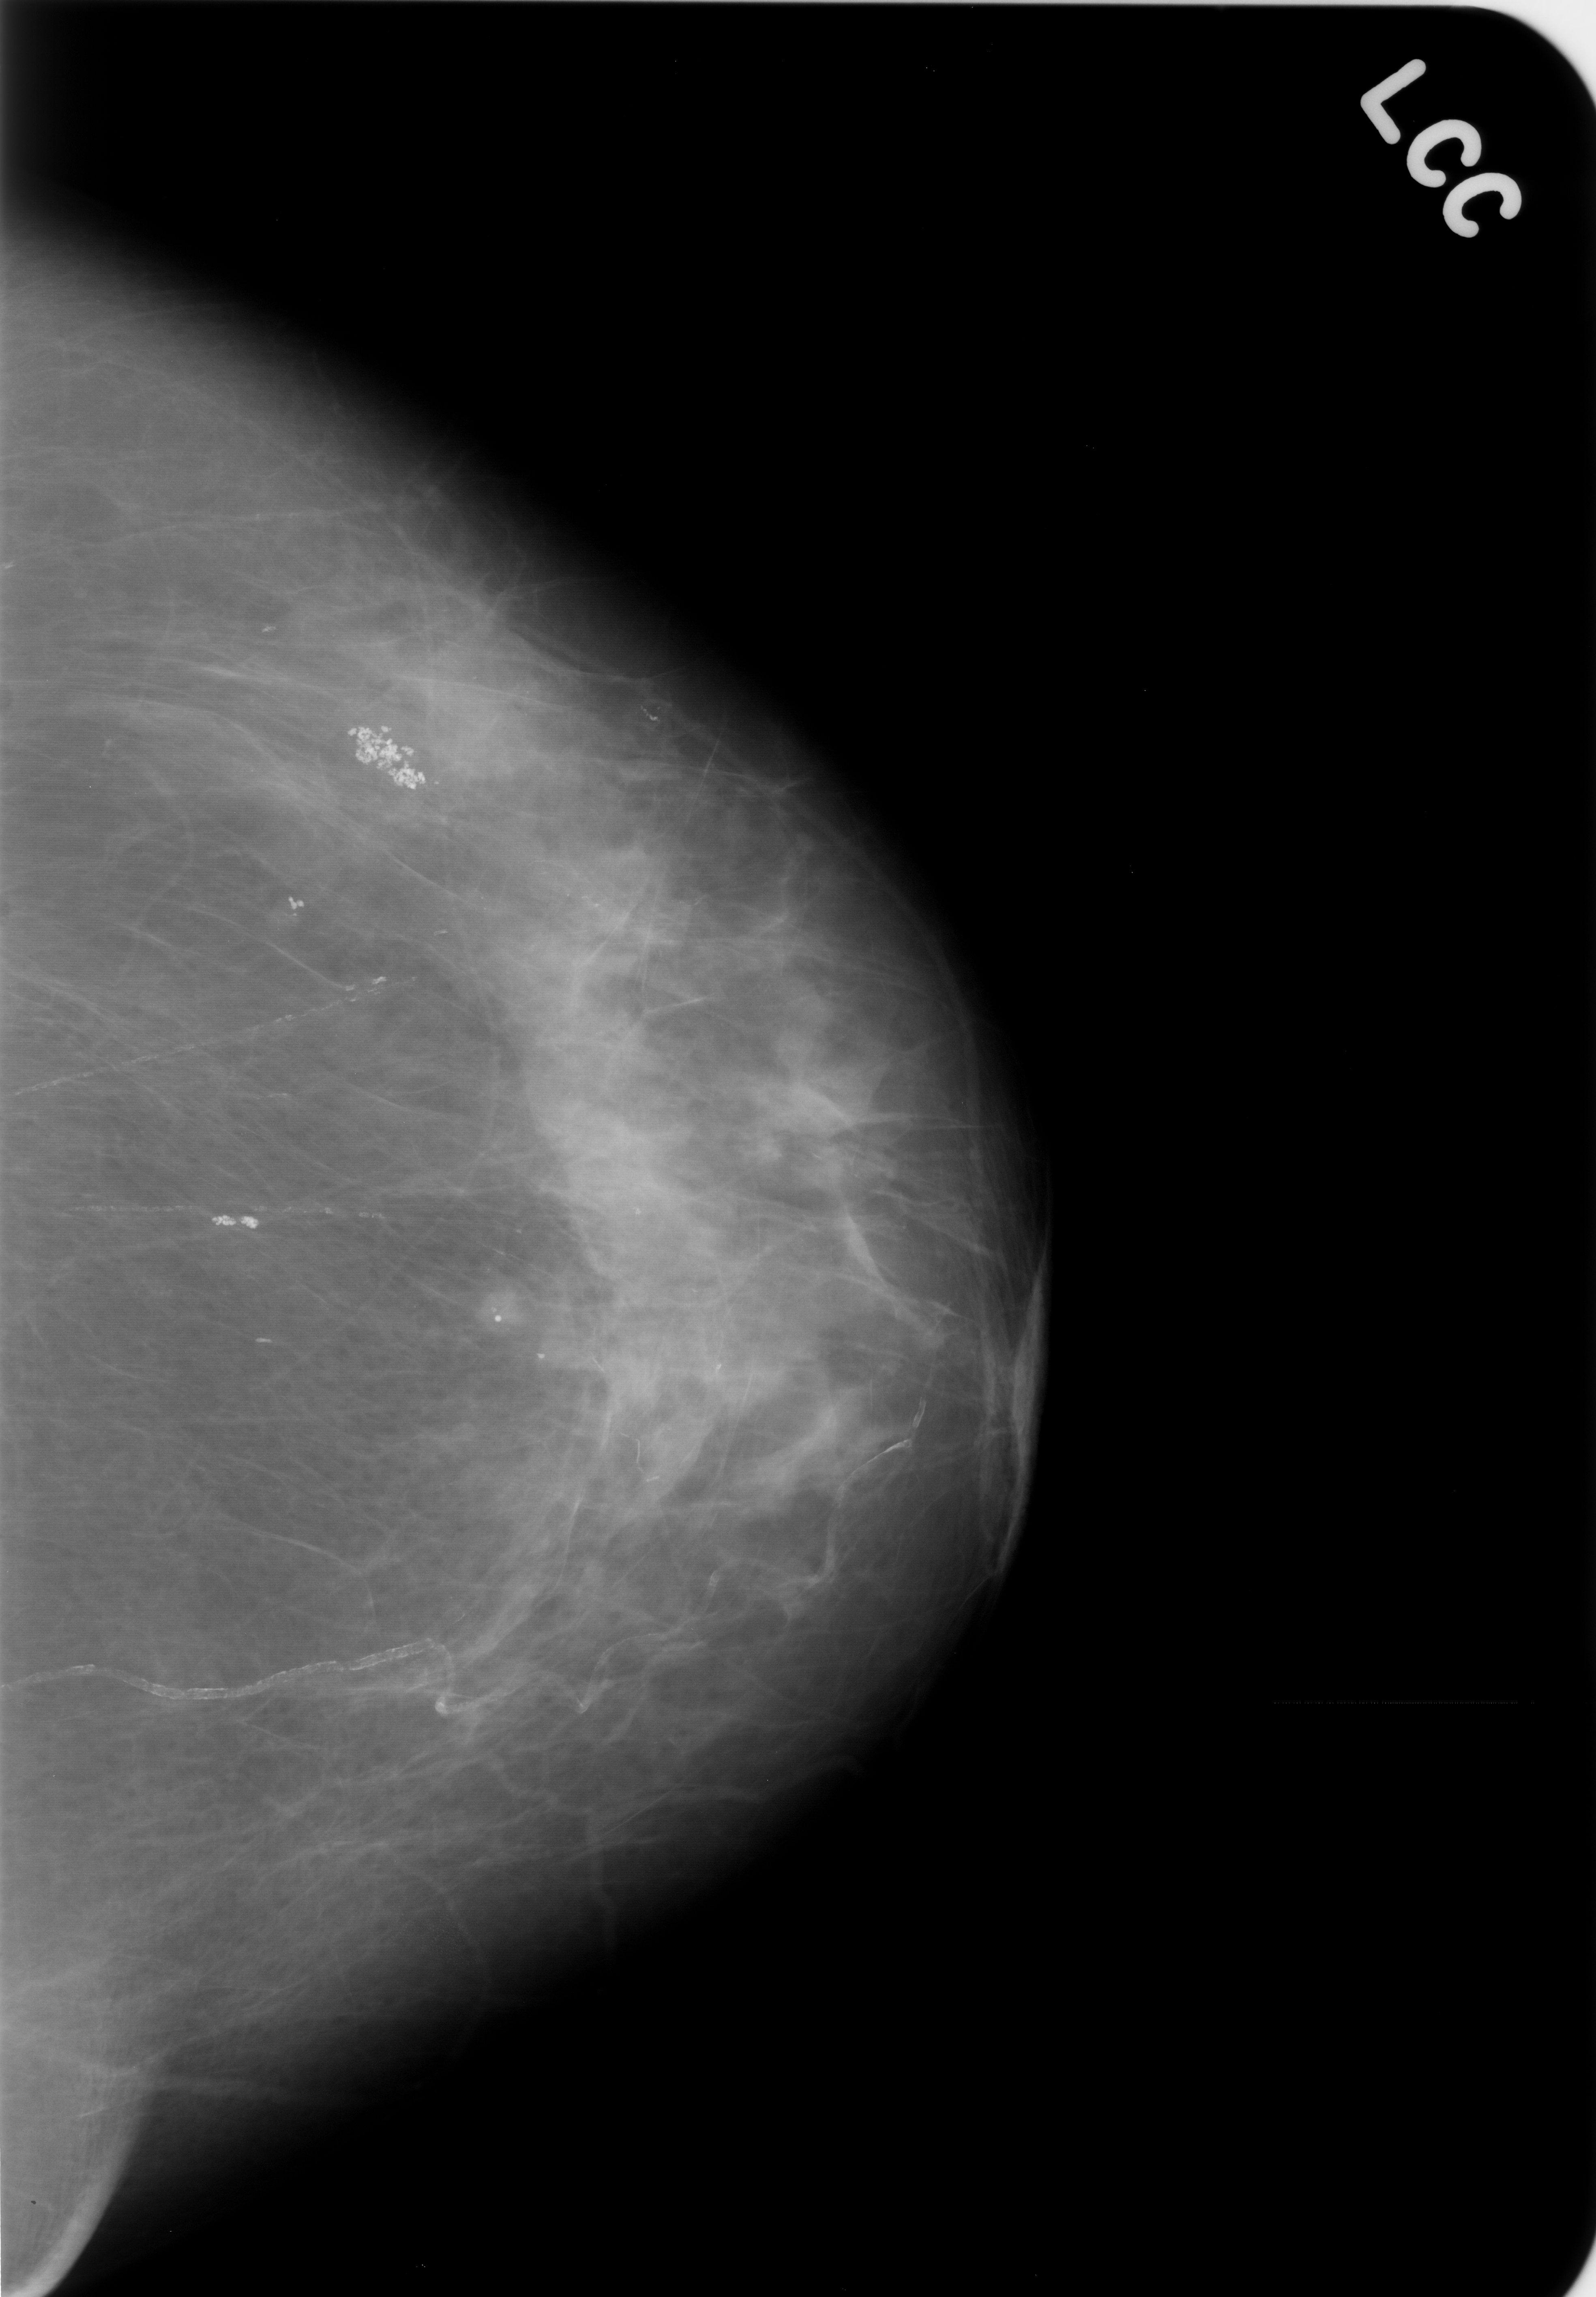
Digitized screen-film mammogram; left breast; CC view; 1596 × 2297 image matrix.
Expert-marked regions of interest on this image (one box per marked abnormality):
- Finding 1 of 2: calcifications, morphology pleomorphic, distribution clustered; BI-RADS assessment category 4; pathology result (as recorded, not read from the image): benign: bounding box <175,1164,319,1266> (left, top, right, bottom; pixels)
- Finding 2 of 2: calcifications, morphology amorphous, distribution clustered; BI-RADS assessment category 4; pathology (as recorded): benign: <301,668,475,854>